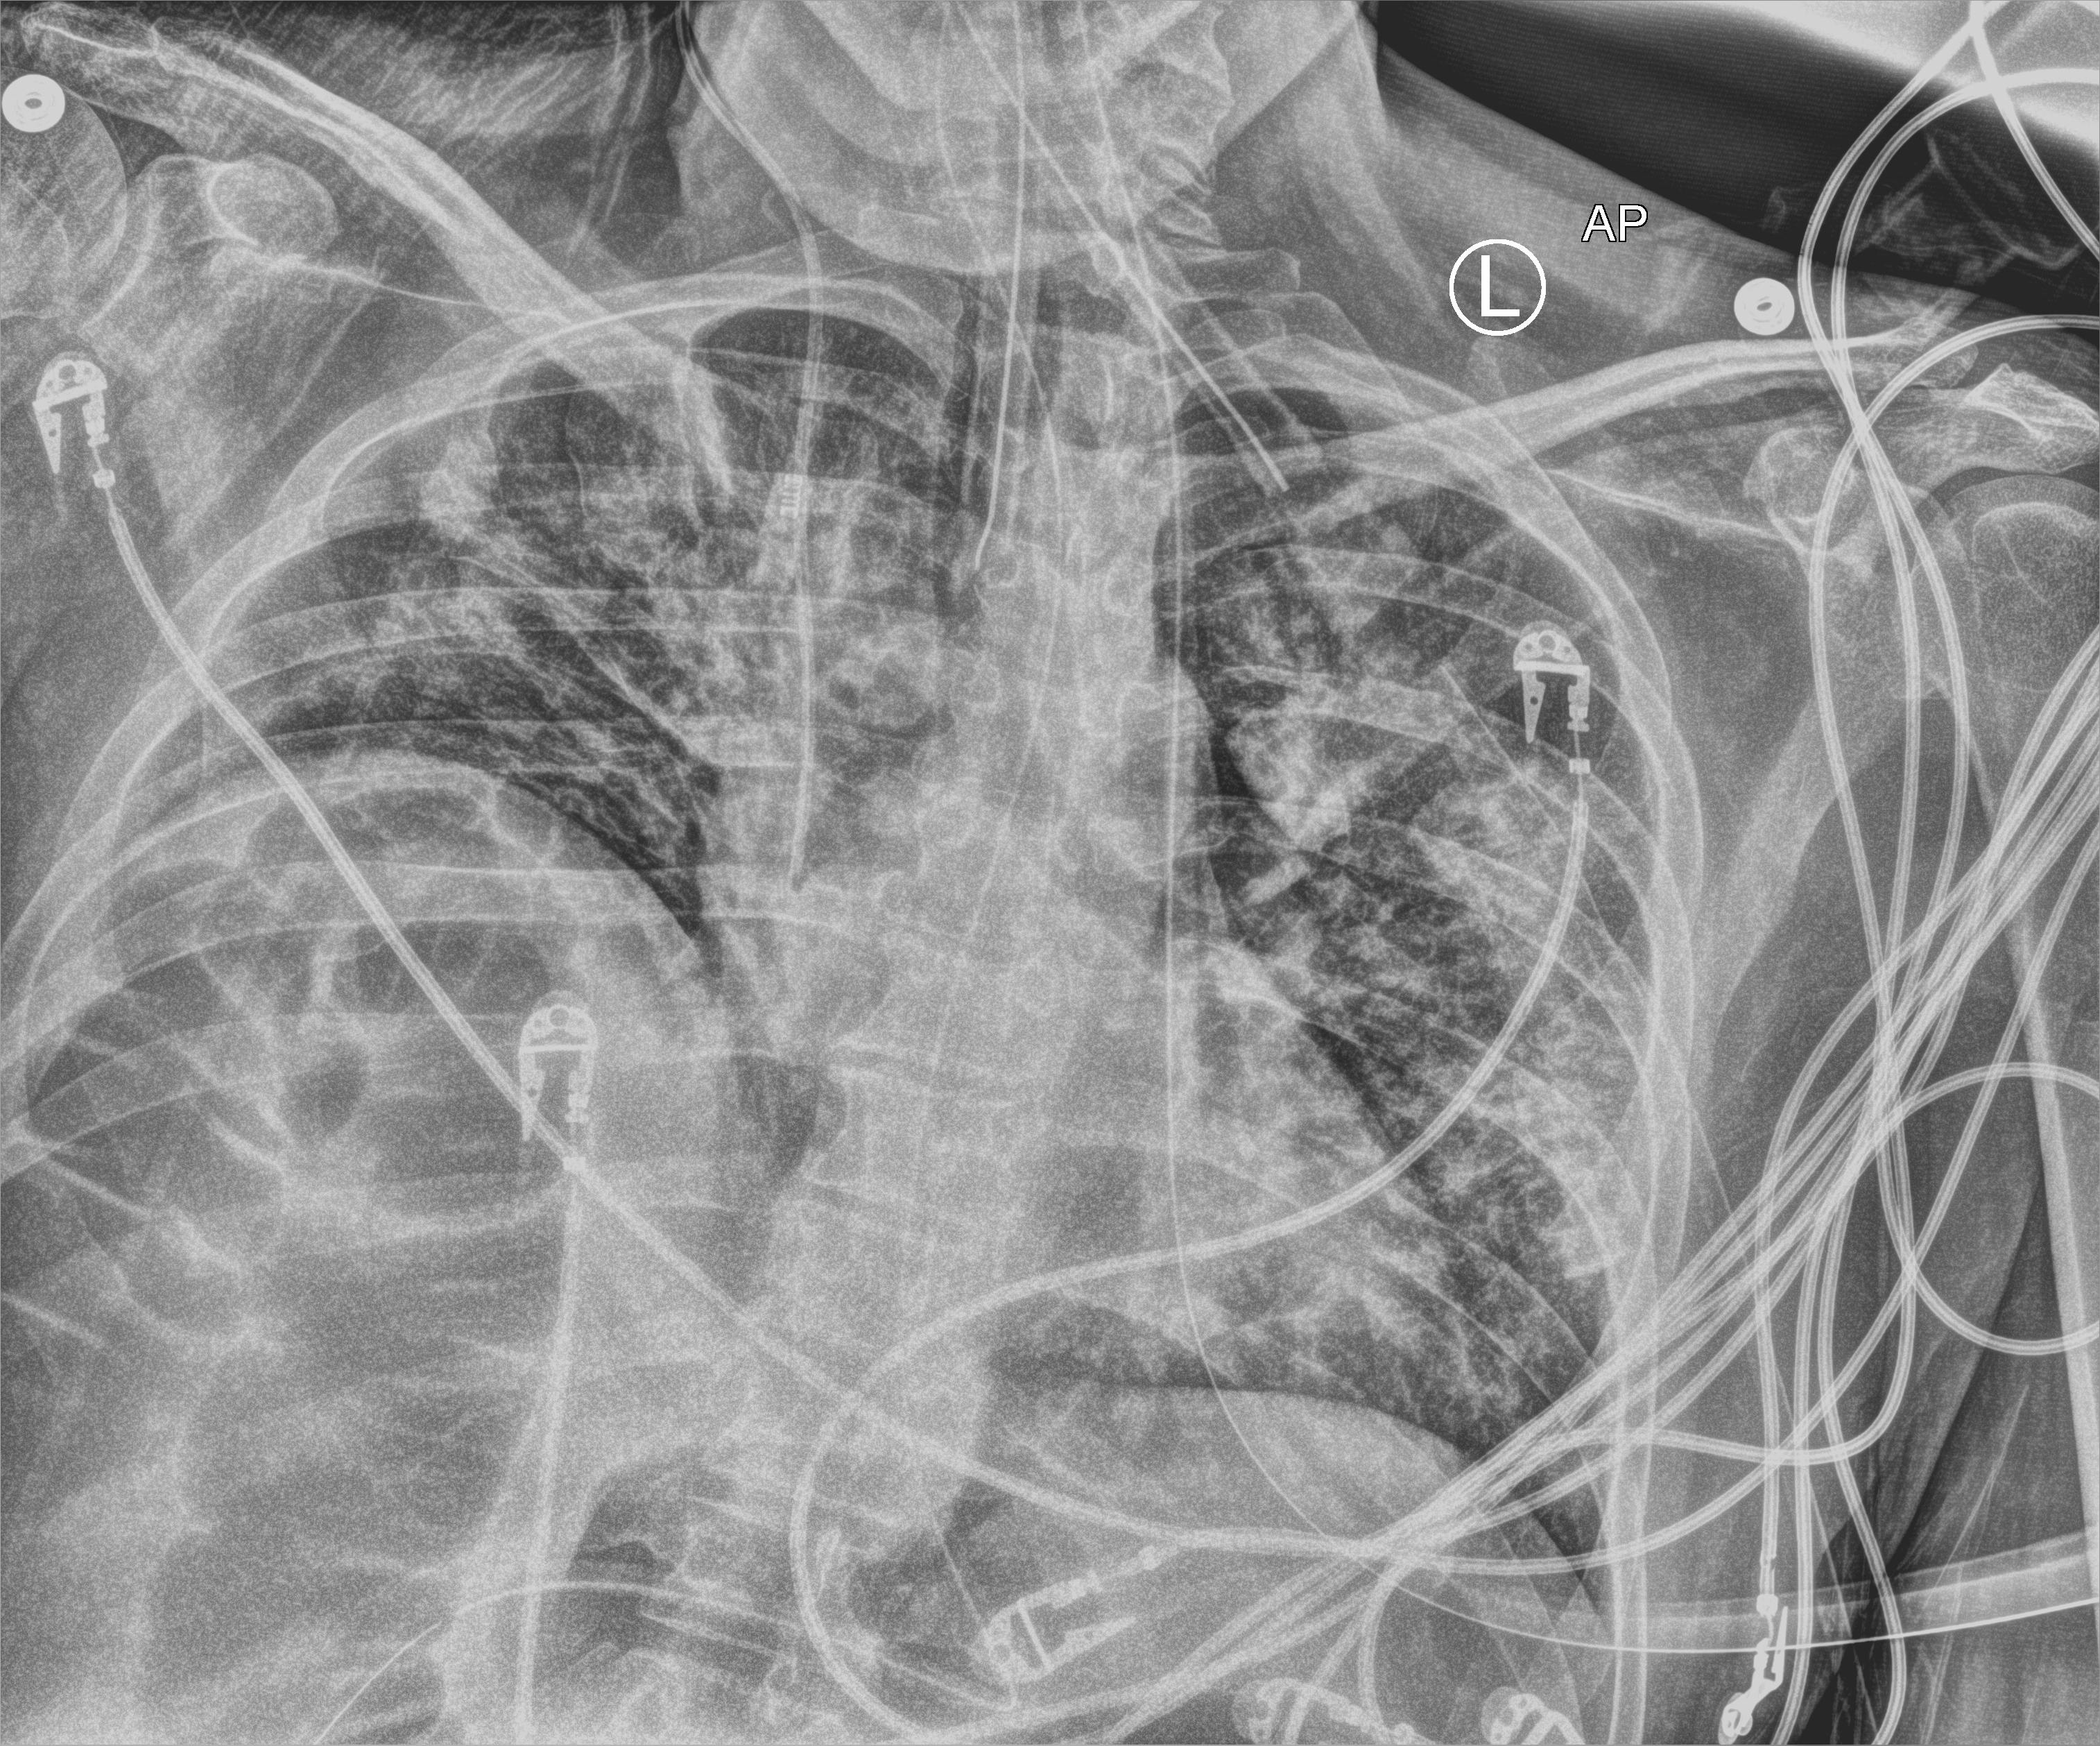
Chest X-ray (portable); anteroposterior (AP) projection. Male patient hospitalised with COVID-19, age 18–59 years.
Hospital-stay facts (about this admission, not read from this image; timing relative to this image not recorded): chronic kidney disease (admission record): no; length of hospital stay: 48 days; mechanically ventilated during this hospital stay: yes.